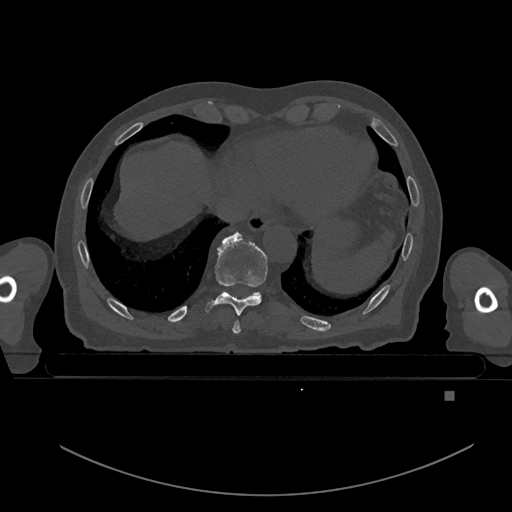
CT including the spine, one axial slice. Slice 140 of 969 in the series (ordered by position). Bone window (W 1800 / L 400 HU). 0.5 mm slice thickness. 512 × 512 image matrix. Male patient, age 82 years. From the clinical record (not read from this slice): primary cancer: prostate; vertebrae with lytic lesions (as recorded): T11, T9, T8, T2.
Annotated regions visible in this slice (semi-automatic segmentation, software-assisted and operator-edited):
- T10 vertebra: bounding box [x1, y1, x2, y2] px = [256, 292, 260, 295]
- T8 vertebra: [232, 320, 241, 334]
- T9 vertebra: [205, 232, 268, 315]